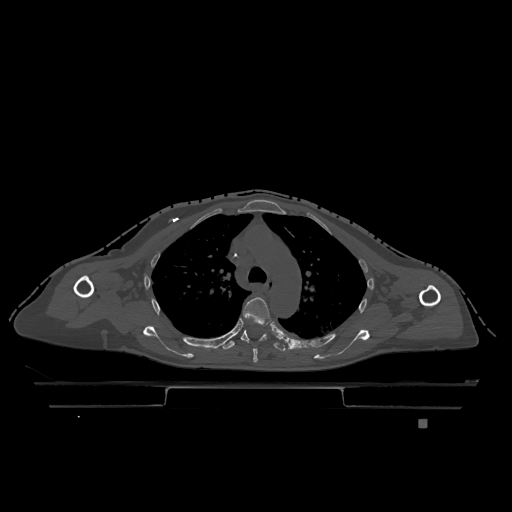
CT including the spine, one axial slice. Slice 859 of 1317 in the series (ordered by position). Bone window (W 1800 / L 400 HU). 0.5 mm slice thickness. 512 × 512 image matrix, field of view 500 × 500 mm. Patient: female, 74 years. Case-level facts recorded for this patient, not image findings: primary cancer: lung; vertebrae with lytic lesions (as recorded): T1, T4, T5, T6, L4, L5.
Annotated regions visible in this slice (semi-automatically segmented with operator editing):
- T4 vertebra: bounding box [x1, y1, x2, y2] px = [240, 297, 271, 363]
- T5 vertebra: [221, 329, 286, 352]